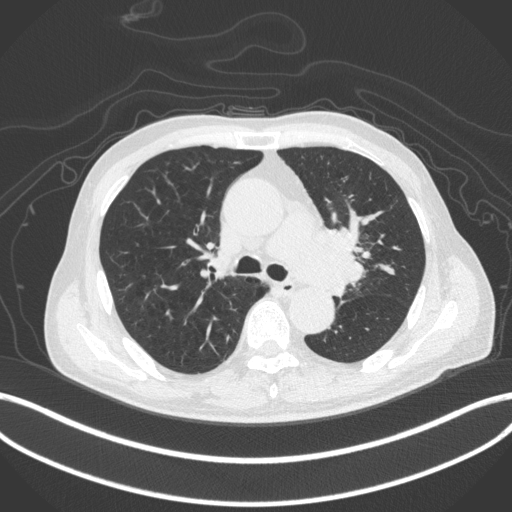
Chest CT, one axial slice; slice 279 of 420 in the series (ordered by position); reconstruction kernel B31f; 120 kVp; lung window (W 1500 / L -600 HU); 1 mm slice thickness; 512 × 512 image matrix. Patient: male, 77 years. From the clinical record (not read from this slice): clinical TNM (as recorded): T3 N1 M0.
Outlined on this slice (rectangle marked by the reading radiologist):
- lung tumour (recorded histology: adenocarcinoma): bounding box <303,221,369,296> (left, top, right, bottom; pixels)